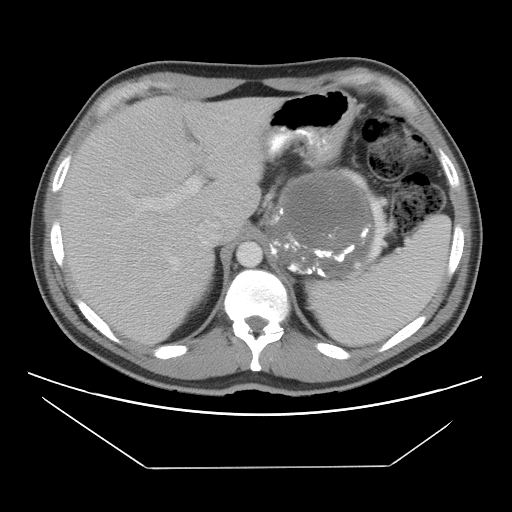
Contrast-enhanced abdominal CT, one axial slice. Slice 77 of 131 in the series (ordered by position). Reconstruction kernel STANDARD. Soft-tissue window (W 400 / L 40 HU). 5 mm slice thickness. 512 × 512 image matrix, field of view 396 × 396 mm. Patient: male, 44 years. From the clinical record (not read from this slice): diagnosis: adrenocortical carcinoma; tumour side: left adrenal; tumour size at pathology: 15.5 cm; Ki-67 index: 6 %; stage (as recorded): 2.
Outlined on this slice (semi-automatically segmented with operator editing):
- mass: bounding box [x1, y1, x2, y2] px = [268, 170, 372, 276]